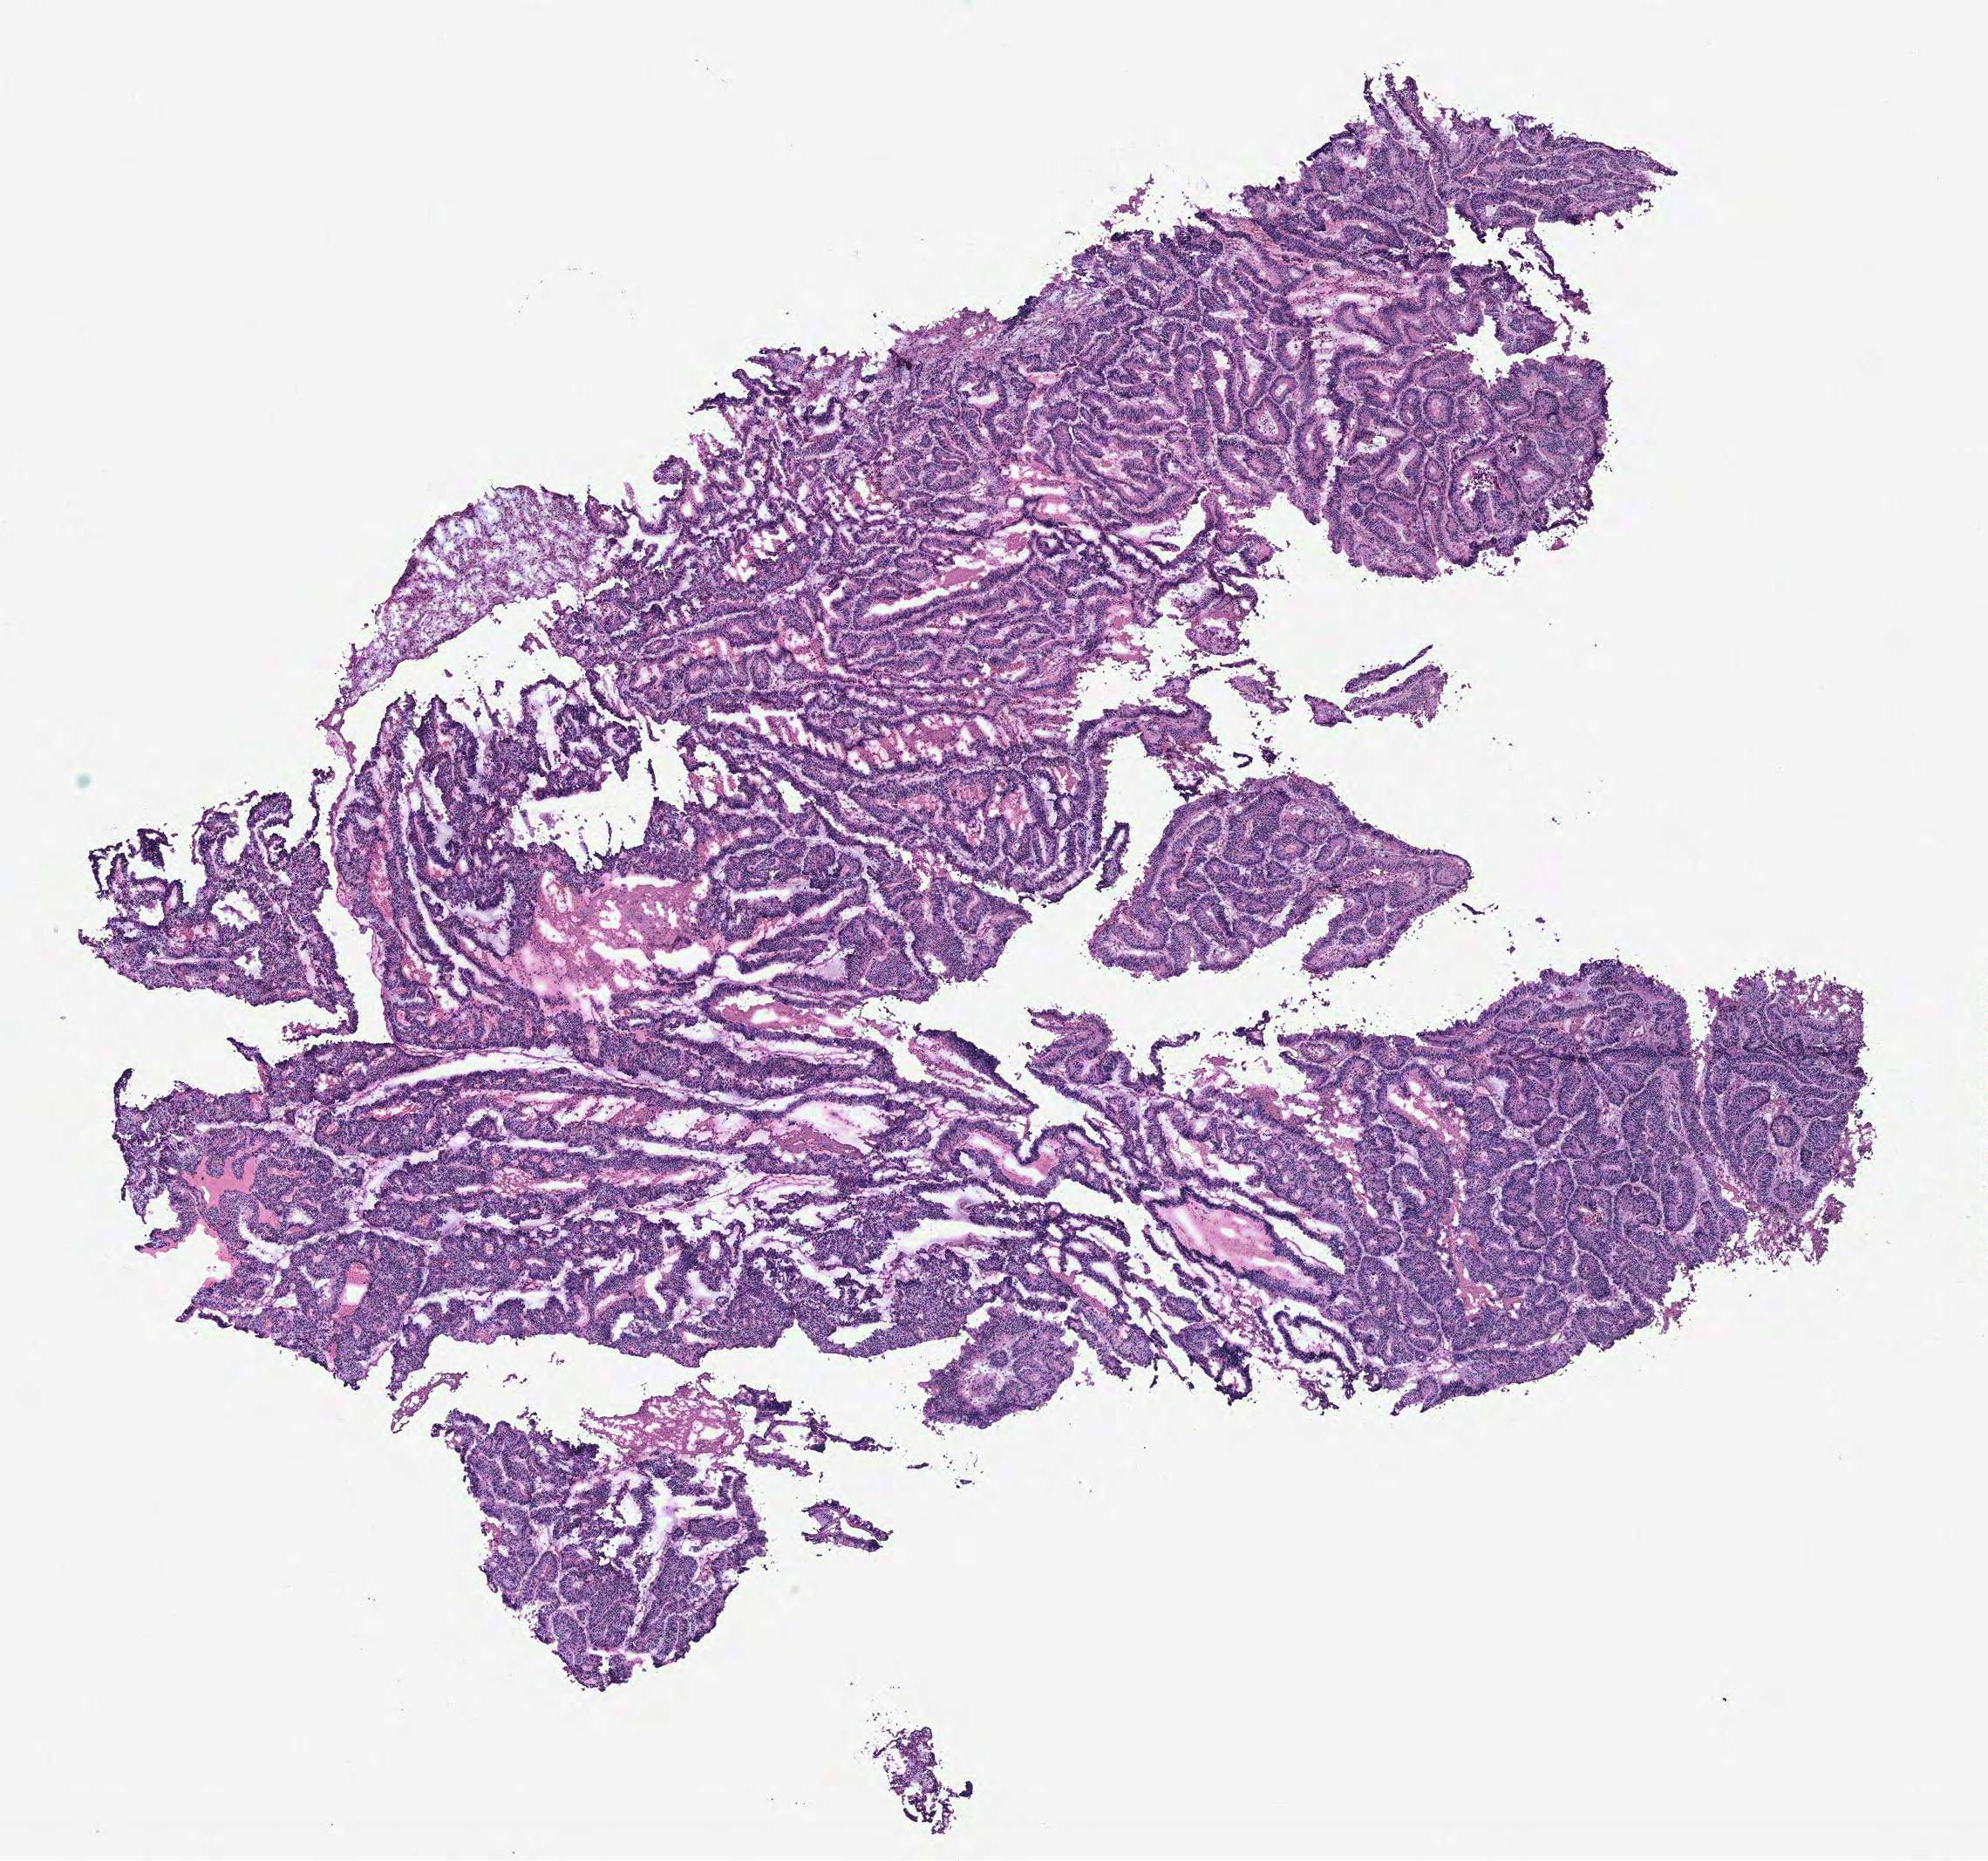
H&E whole-slide image, shown as a low-resolution overview of the whole scanned area (about 9.1 x 8.5 mm, acquisition: 40x scan). Tumour tissue sample, colon. Male, 50 y/o.
* diagnosis: Adenocarcinoma, NOS
* primary tumour site (as recorded): colon
* AJCC pathologic stage: IV